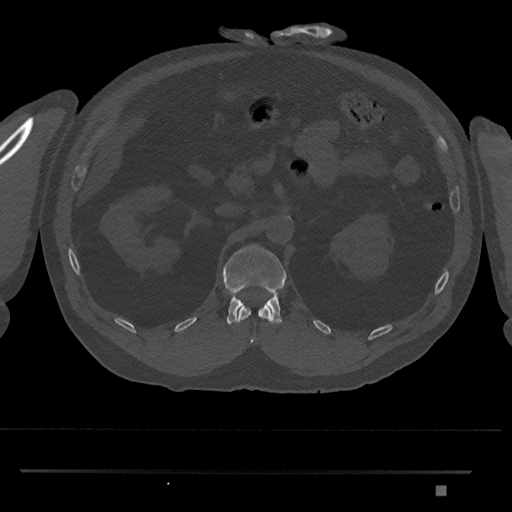
CT including the spine, one axial slice; position 849 of 1134 along the scan axis; 120 kVp; bone window (W 1800 / L 400 HU); 0.5 mm slice thickness; 512 × 512 image matrix. Patient: male, 65 years. From the clinical record (not read from this slice): primary cancer: prostate.
Outlined on this slice (semi-automatically segmented with operator editing):
- L1 vertebra: box from (x=223, y=244) to (x=287, y=325) px
- T12 vertebra: (x=238, y=305)–(x=272, y=344)